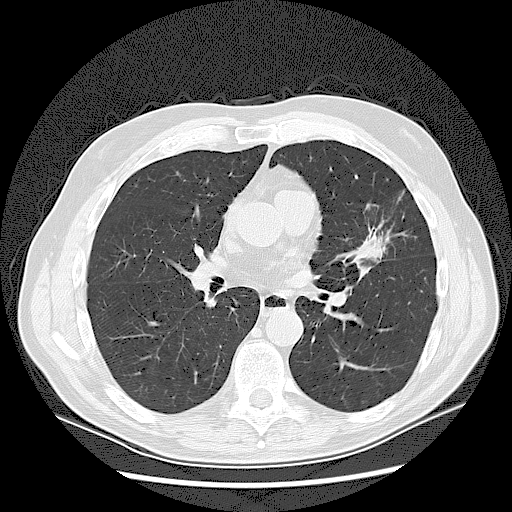
Low-dose screening chest CT, one axial slice; slice 69 of 132 in the series (ordered by position); lung window (W 1500 / L -600 HU); 2.5 mm slice thickness; 512 × 512 image matrix, field of view 380 × 380 mm.
Outlined on this slice (manually delineated by an expert):
- lesion 1 (tumor, upper lobe of left lung): bounding box [x1, y1, x2, y2] px = [356, 241, 385, 264]